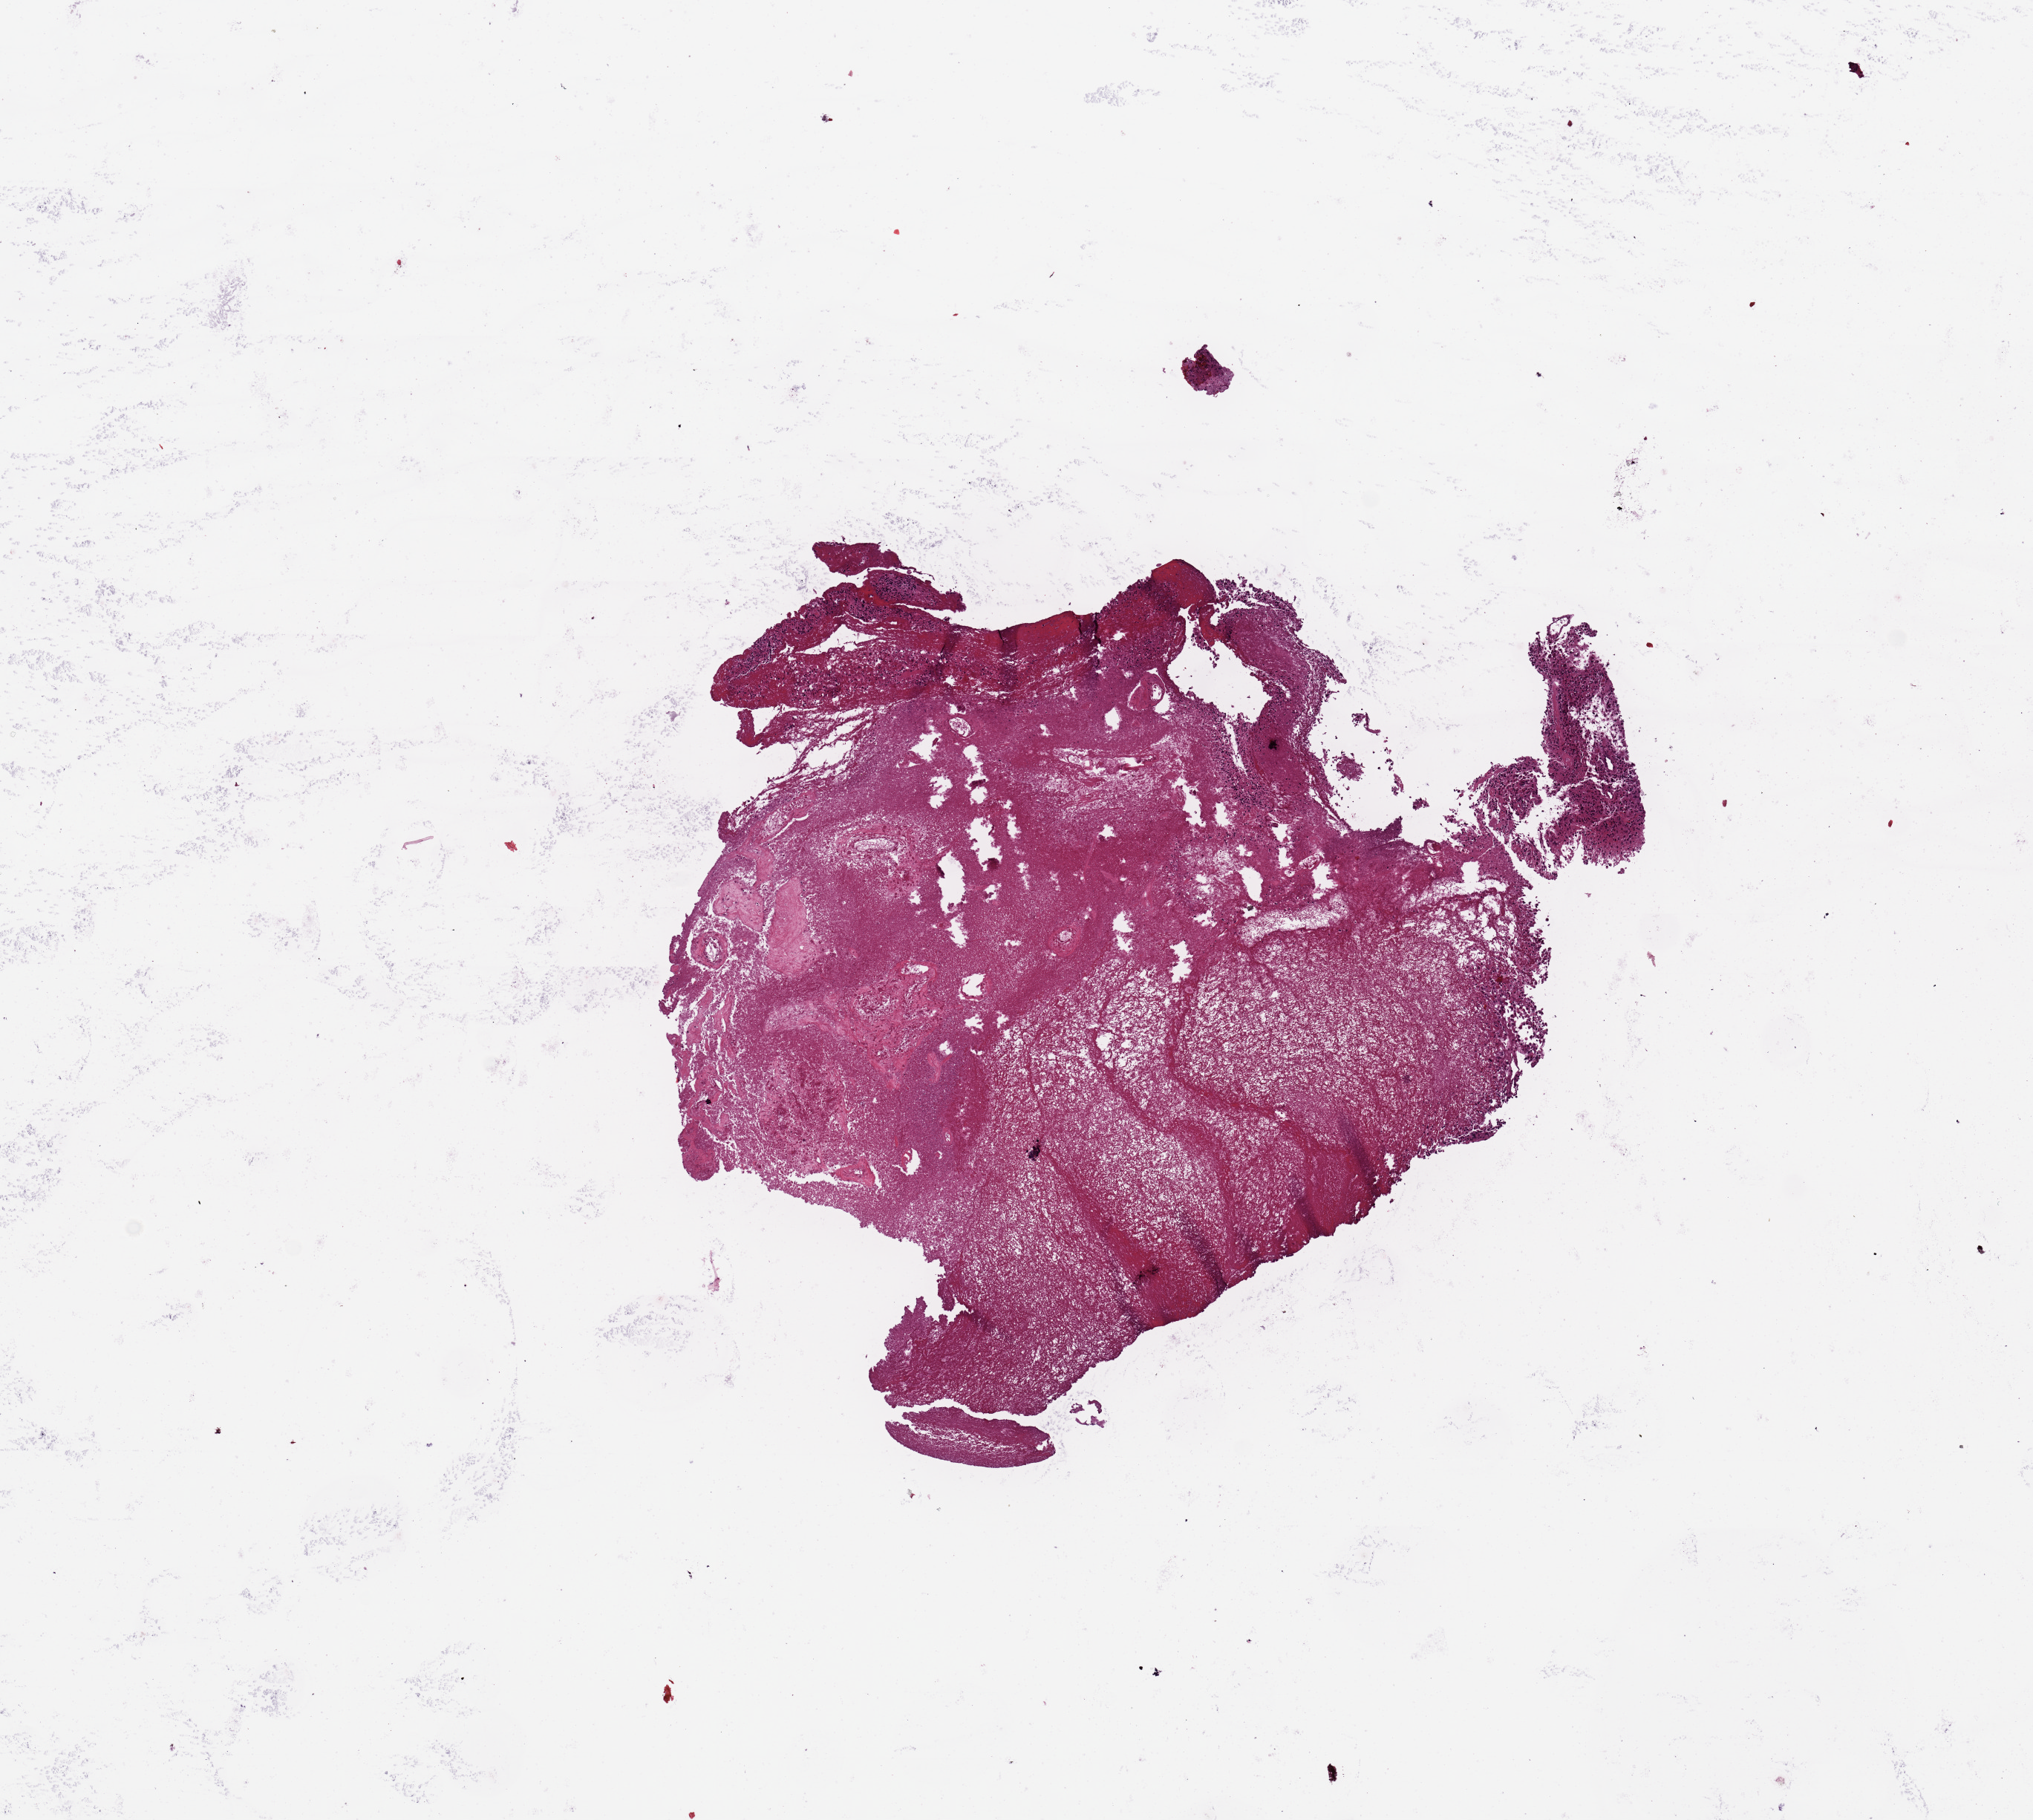
Digitized H&E tissue section (whole slide), a low-resolution overview of the entire scanned area, about 10.8 x 9.7 mm (acquisition: 20x scan); tumour tissue sample, sampled site: brain. Male, 64 y/o. Pathologist review of this section (percent, as recorded): tumour nuclei 30%, necrosis 80%.
Diagnosis: Glioblastoma. Primary tumour site (as recorded): temporal lobe.